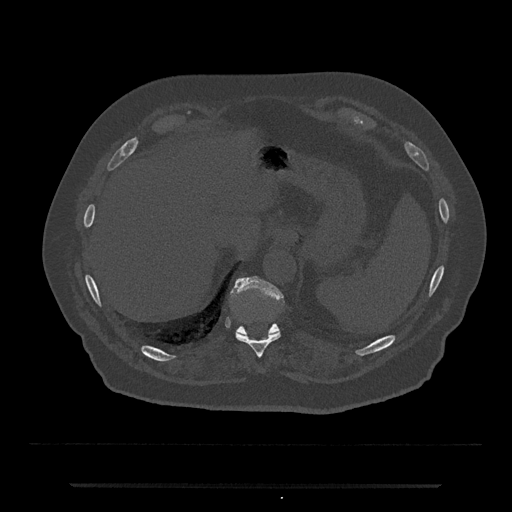
CT including the spine, one axial slice; slice 687 of 797 in the series (ordered by position); reconstruction kernel Br40s/3; 120 kVp; bone window (W 1800 / L 400 HU); 0.5 mm slice thickness; 512 × 512 image matrix, field of view 434 × 434 mm. Male patient, age 80 years. Case-level facts recorded for this patient, not image findings: primary cancer: prostate.
Structures marked on this image (semi-automatically segmented with operator editing):
- T10 vertebra: bounding box (x1, y1, x2, y2) in pixels: (235, 332, 281, 358)
- T11 vertebra: (231, 276, 283, 335)